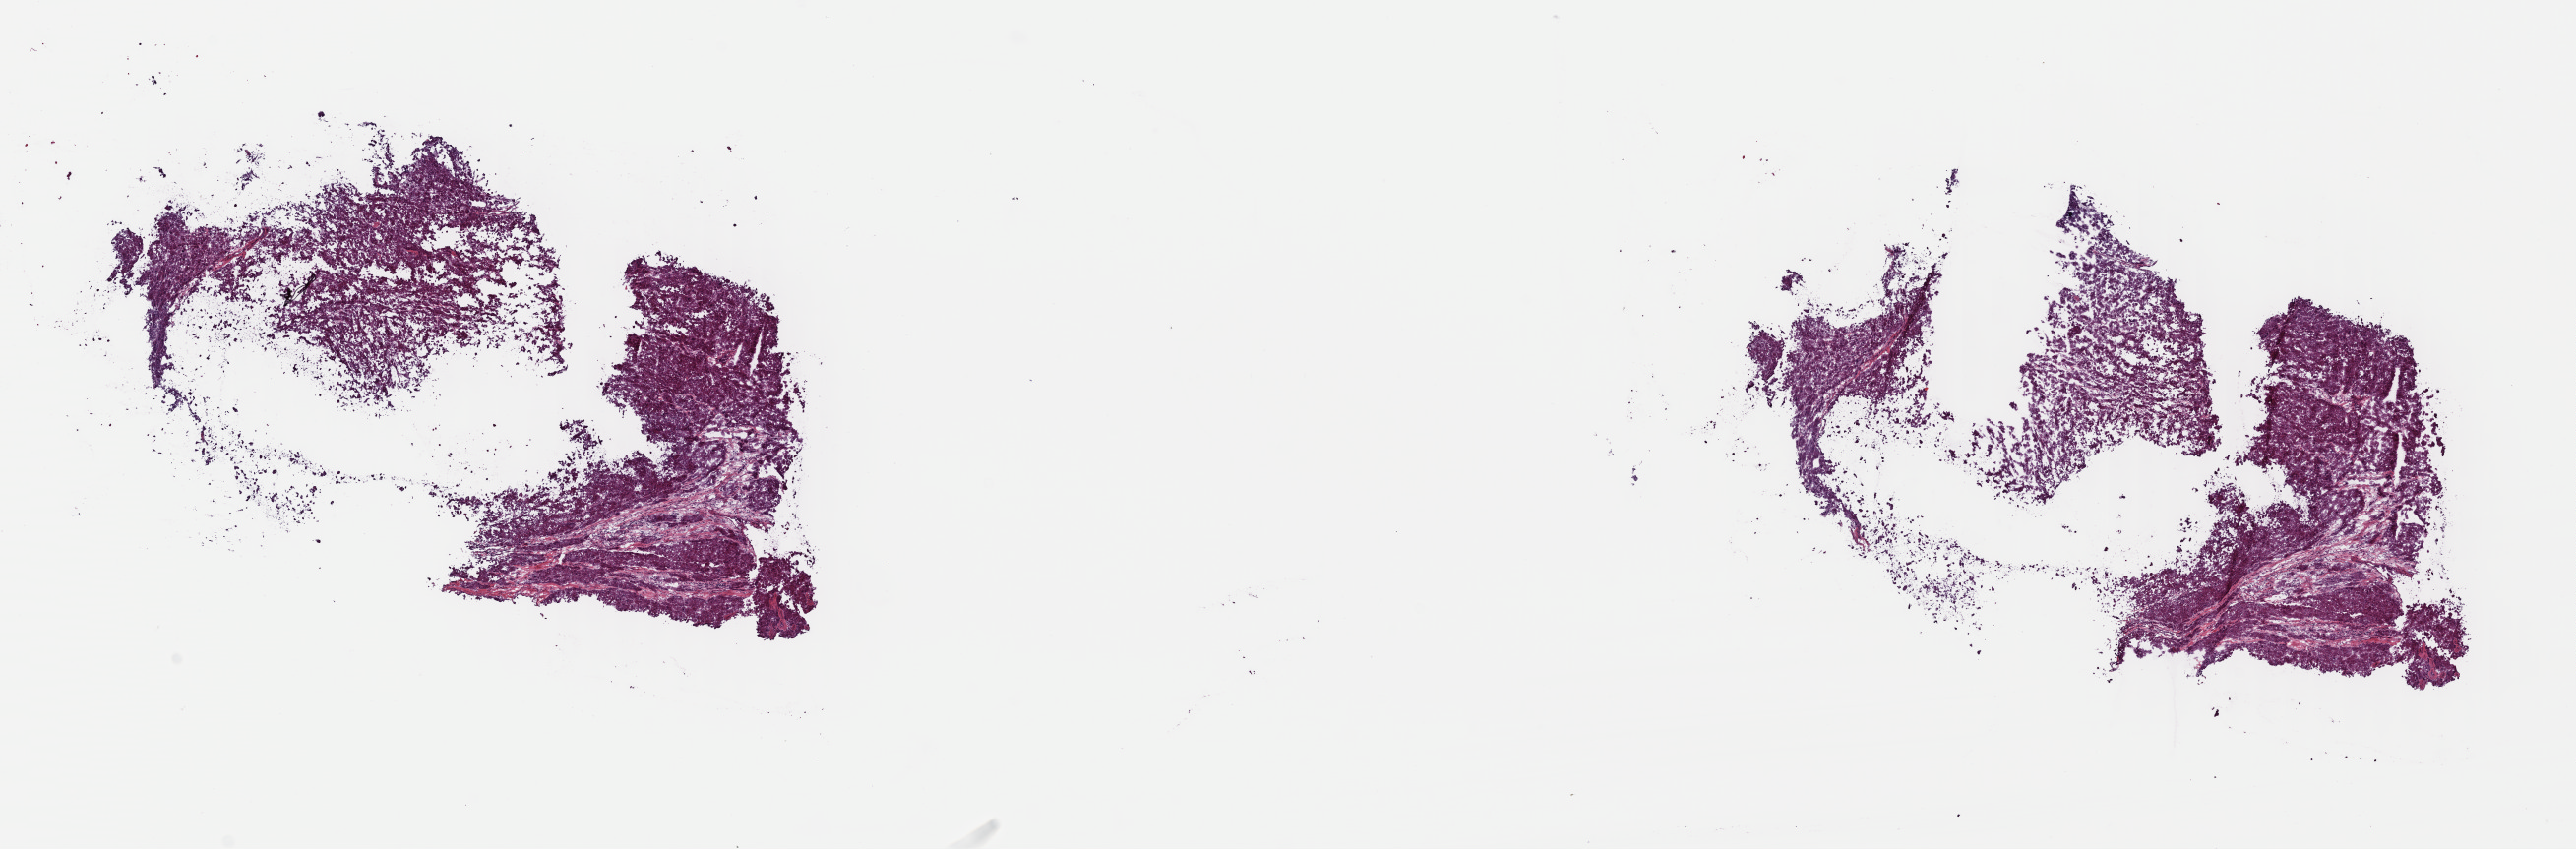
Whole-slide histology image, Hematoxylin and eosin (H&E) stained — whole scanned area (about 20.6 x 6.8 mm, acquisition: 40x scan) shown as a low-resolution overview. Frozen section from the top of the tissue portion. Adrenal cortex, primary tumour sample. Patient: female, age at initial diagnosis 37 years.
Histologic diagnosis: Adrenal cortical carcinoma (cortex of adrenal gland).